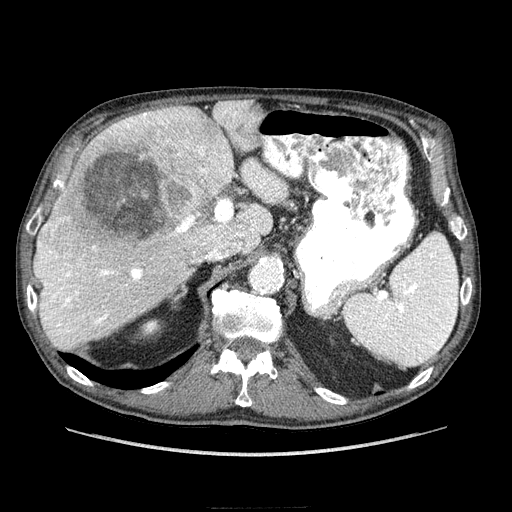
Contrast-enhanced abdominal CT (liver protocol), one axial slice; position 155 of 218 along the scan axis; reconstruction kernel STANDARD; 100 kVp; soft-tissue window (W 400 / L 40 HU); 512 × 512 image matrix. From the clinical record (not read from this slice): diagnosis: hepatocellular carcinoma (patient treated with transarterial chemoembolisation; whether this scan precedes or follows treatment is not stated here); TNM stage (as recorded): Stage-IIIA; Child-Pugh class: A; tumour differentiation: well differentiated; tumour size: 20 cm.
Structures marked on this image (semi-automatically segmented with operator editing):
- liver parenchyma outside the tumour (the mass and vessels are separate outlines, so this box may not span the whole liver): bounding box [x1, y1, x2, y2] px = [34, 100, 287, 348]
- mass: [47, 105, 235, 263]
- liver vessels: [37, 108, 283, 335]